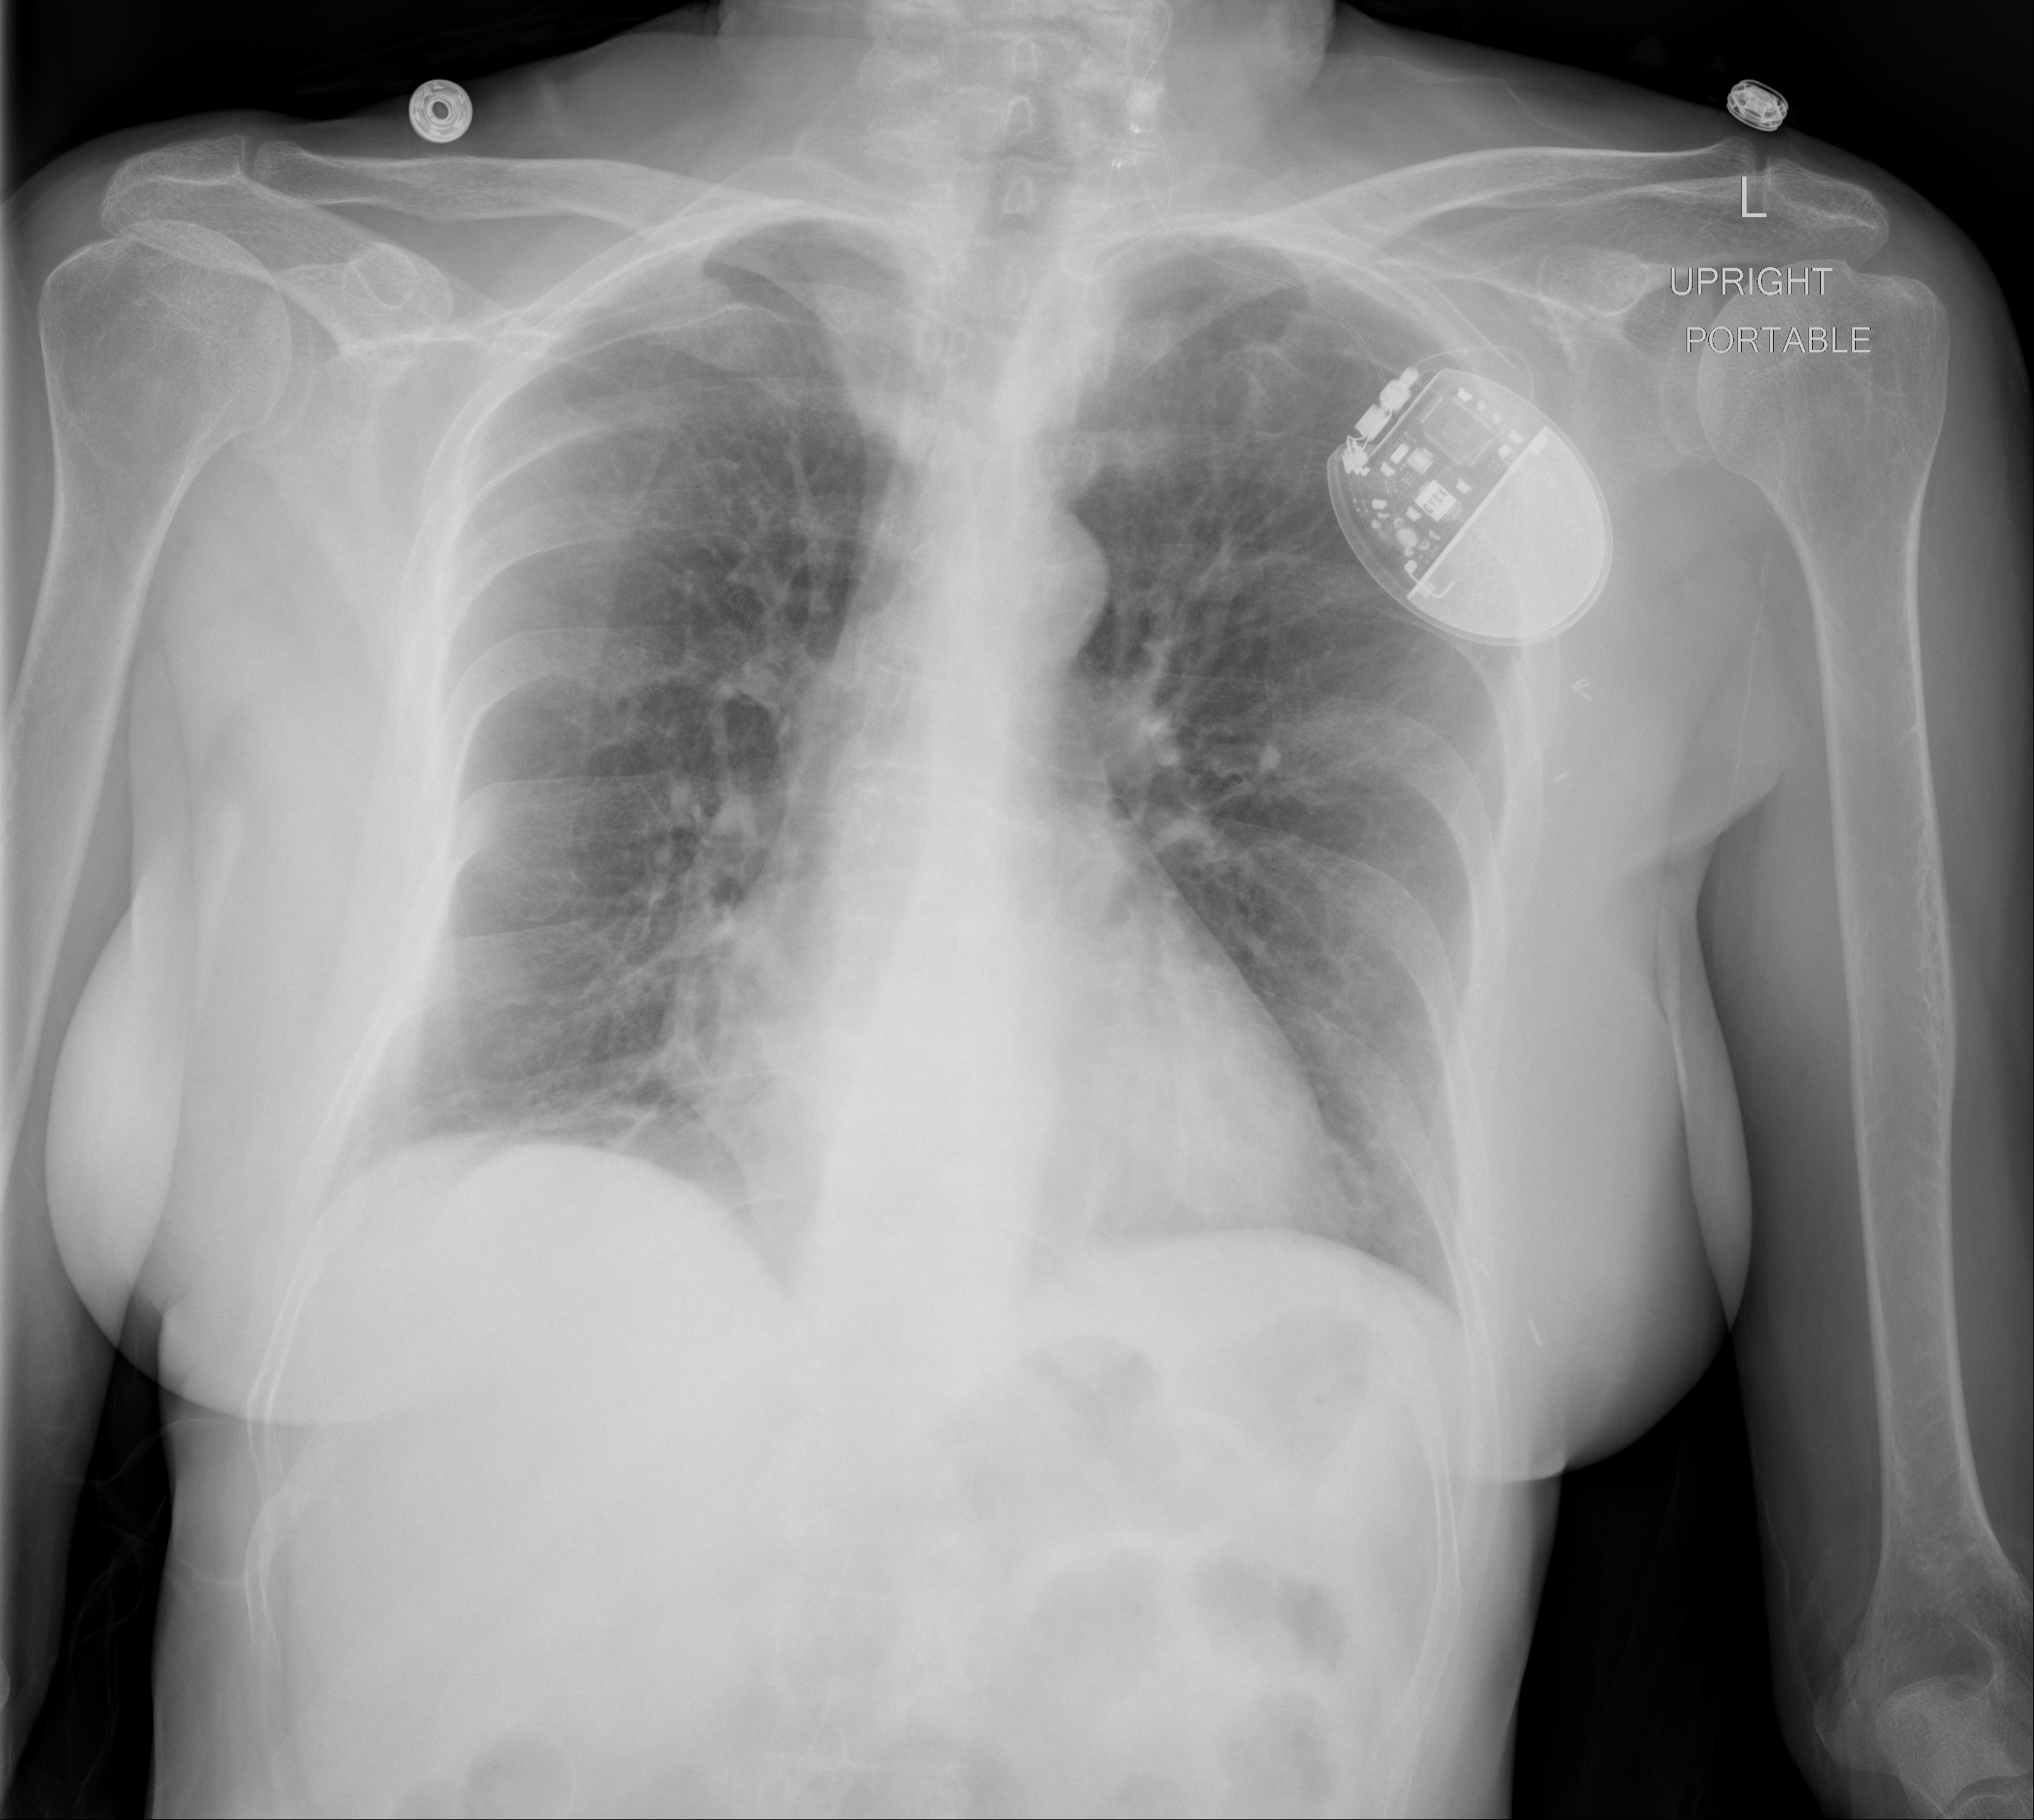
Portable chest radiograph, AP projection. Female patient, age 70 years; imaged 1 day after the COVID-19 diagnosis.
Radiologist's key findings for this exam: Right basilar atelectasis.